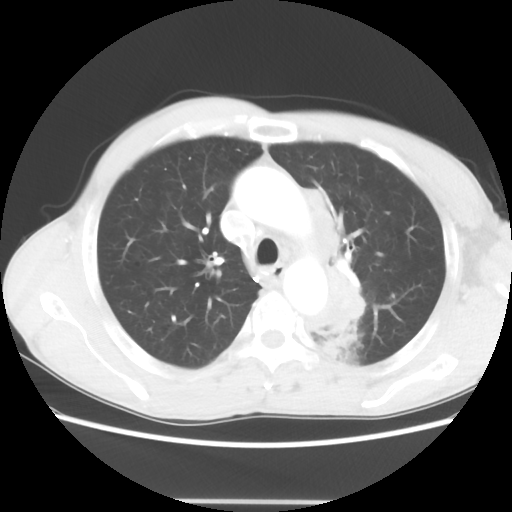
Chest CT, one axial slice; position 46 of 62 along the scan axis; reconstruction kernel STANDARD; 100 kVp; lung window (W 1500 / L -600 HU); 5 mm slice thickness; 512 × 512 image matrix, field of view 360 × 360 mm. Patient: male, 61 years. From the clinical record (not read from this slice): clinical TNM (as recorded): T3 N1 M1.
Structures marked on this image (rectangle marked by the reading radiologist):
- lung tumour (recorded histology: adenocarcinoma): bounding box [x1, y1, x2, y2] px = [304, 176, 371, 364]